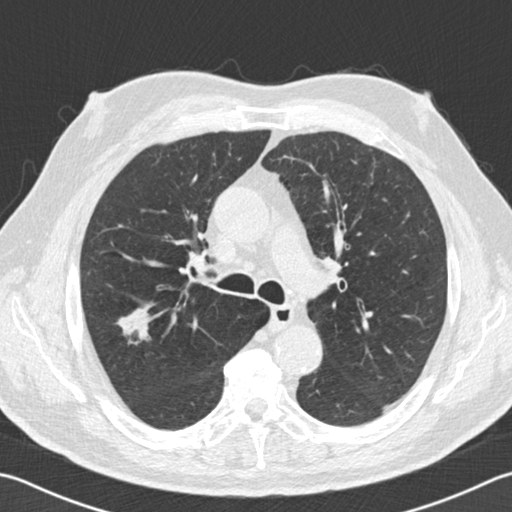
Low-dose screening chest CT, one axial slice; slice 109 of 162 in the series (ordered by position); 120 kVp; lung window (W 1500 / L -600 HU); 2 mm slice thickness; 512 × 512 image matrix, field of view 346 × 346 mm.
Outlined on this slice (outlined manually by an expert reader):
- lesion 1 (tumor, upper lobe of right lung): box from (x=117, y=307) to (x=152, y=344) px